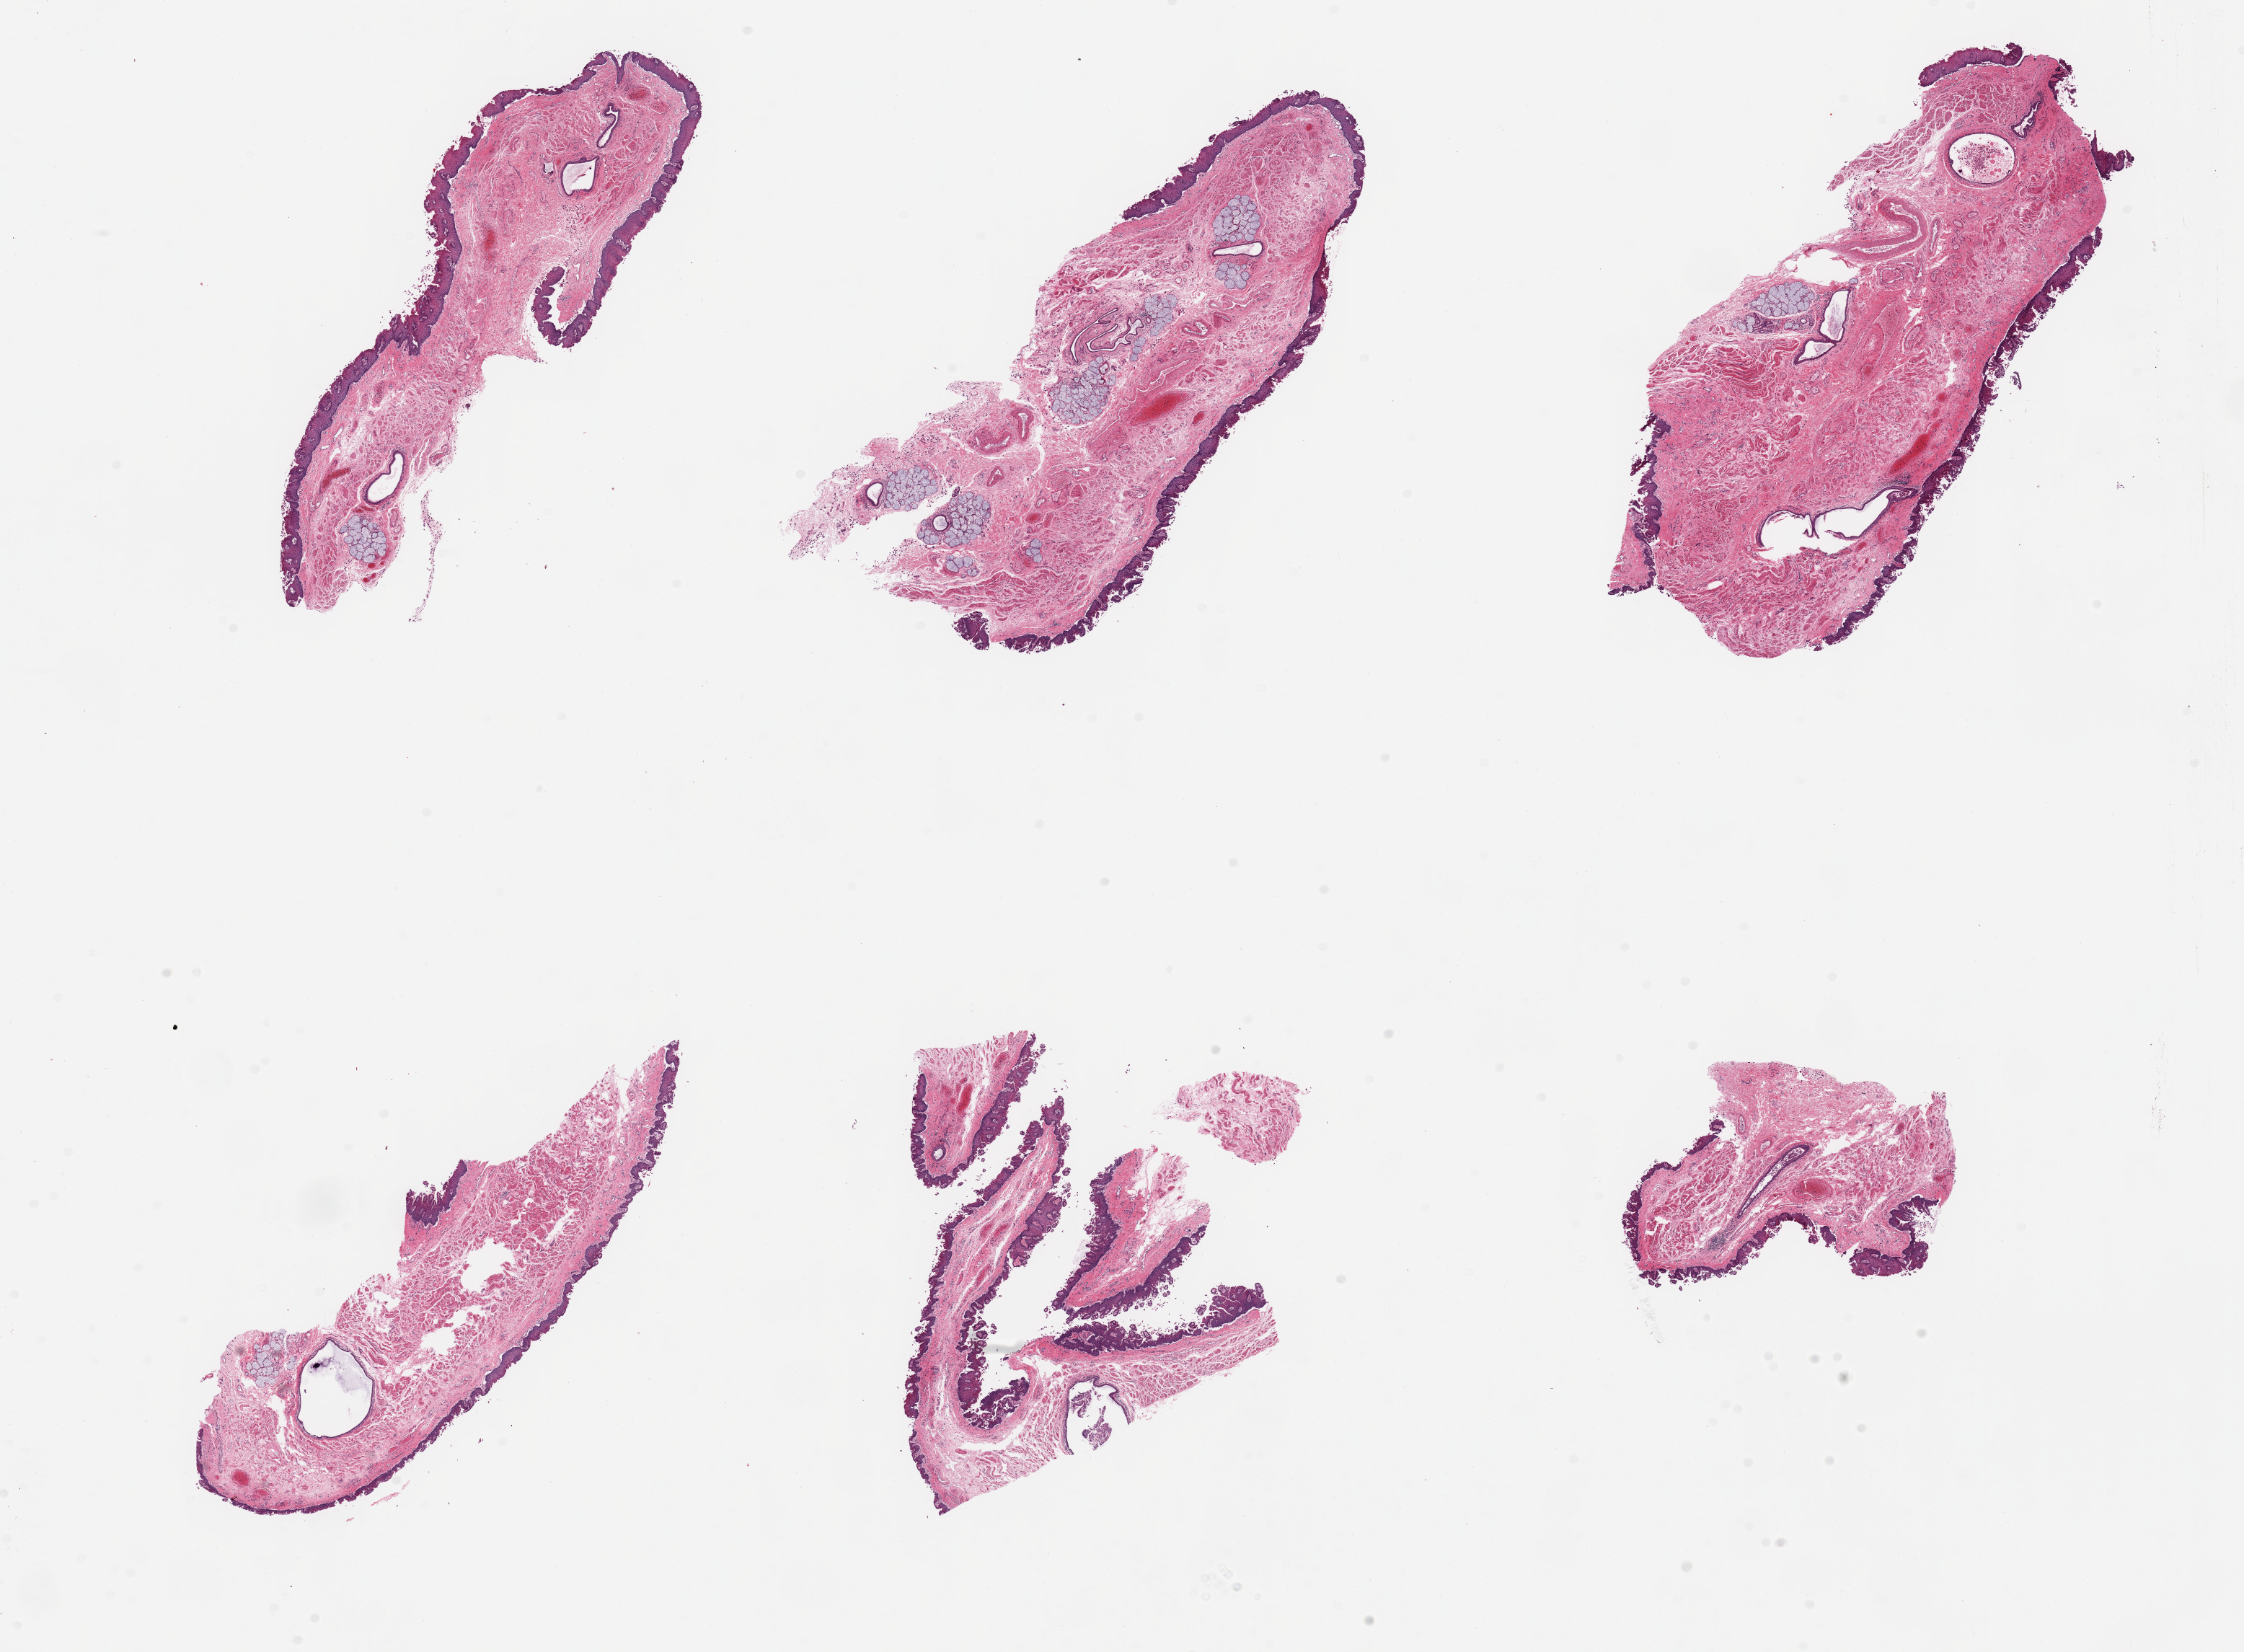
Digitized hematoxylin and eosin (H&E)-stained section, brightfield, low-resolution overview of the scanned area, about 24.6 x 18.1 mm (from a 20x scan), PAXgene-fixed paraffin-embedded (PFPE) section, sampled site (target tissue): esophageal mucous membrane, tissue donor sample. Male donor.
Review note (as recorded): 6 pieces, squamous mucosa up to ~0.2mm, sloughing; prominent submucosal mucus glands.